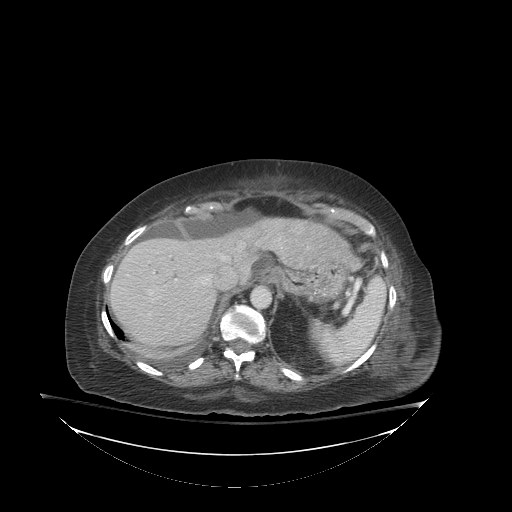
Contrast-enhanced abdominal CT (liver protocol), one axial slice; slice 64 of 81 in the series (ordered by position); reconstruction kernel STANDARD; 140 kVp; soft-tissue window (W 400 / L 40 HU); 2.5 mm slice thickness; 512 × 512 image matrix, field of view 500 × 500 mm. Case-level facts recorded for this patient, not image findings: diagnosis: hepatocellular carcinoma (patient treated with transarterial chemoembolisation; whether this scan precedes or follows treatment is not stated here); TNM stage (as recorded): Stage-I; Child-Pugh class: B; tumour differentiation: well-moderately differentiated; tumour nodularity: uninodular.
Outlined on this slice (semi-automatic segmentation, software-assisted and operator-edited):
- liver parenchyma outside the tumour (the mass and vessels are separate outlines, so this box may not span the whole liver): box from (x=110, y=218) to (x=314, y=352) px
- liver vessels: (x=150, y=257)–(x=224, y=295)